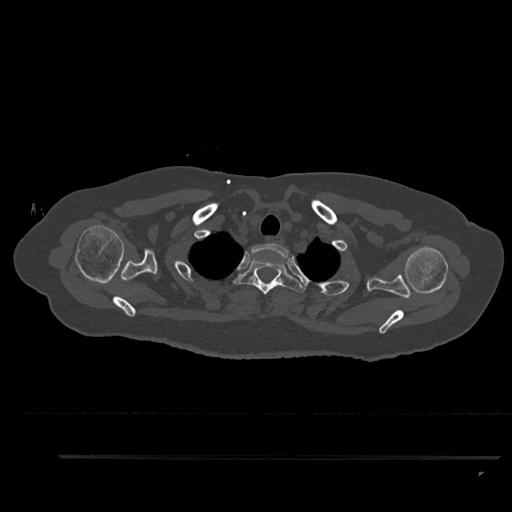
CT including the spine, one axial slice. Slice 732 of 797 in the series (ordered by position). Reconstruction kernel Br40s/3. 120 kVp. Bone window (W 1800 / L 400 HU). 0.5 mm slice thickness. 512 × 512 image matrix. Female patient, age 44 years. From the clinical record (not read from this slice): primary cancer: renal; vertebrae with lytic lesions (as recorded): L1.
Annotated regions visible in this slice (semi-automatically segmented with operator editing):
- T1 vertebra: bounding box (x1, y1, x2, y2) in pixels: (249, 243, 289, 261)
- T2 vertebra: (233, 259, 306, 295)